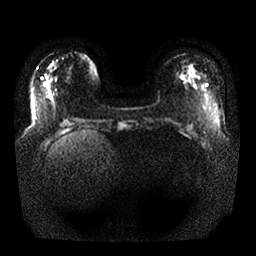
Breast MRI, one axial slice; position 7 of 25 along the scan axis; diffusion-weighted series; image 2 of 4 stored at this slice position (different b-values; order by instance number); 1.5 T; 4 mm slice thickness; 256 × 256 image matrix, field of view 350 × 350 mm. Female patient.
Annotated regions visible in this slice (manually delineated by an expert):
- tumour on diffusion-weighted imaging: bounding box <181,74,185,80> (left, top, right, bottom; pixels)